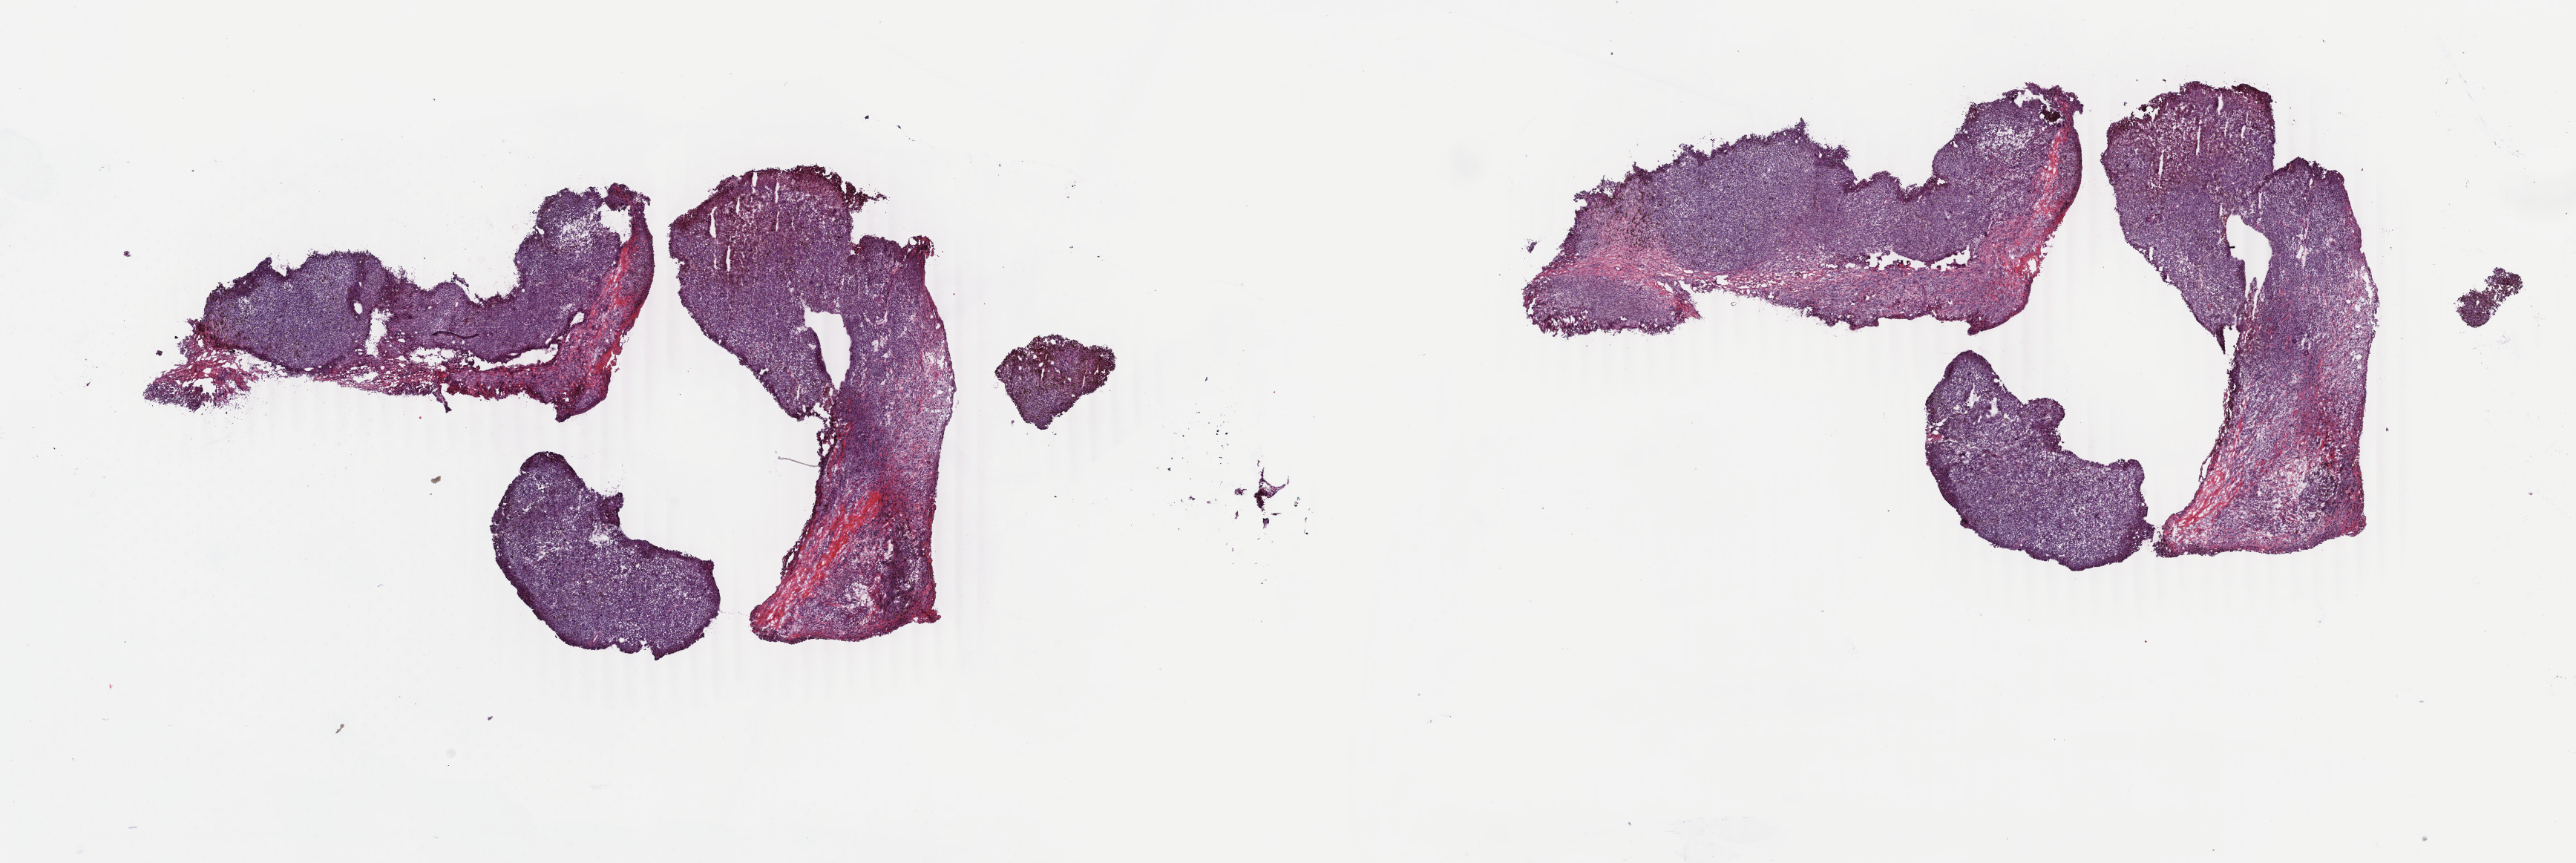
Hematoxylin and eosin (H&E) stained whole-slide image — whole scanned area (about 27.6 x 9.2 mm, from a 40x scan) shown as a low-resolution overview. Frozen section. Metastatic tumour sample, sampled site: connective, subcutaneous and other soft tissues. Male patient; age at initial diagnosis 64 years. Composition of this section per pathologist review: tumour cells 100%, tumour nuclei 91%, normal cells 0%, stromal cells 0%, necrosis 0%. Infiltration values recorded for this section: lymphocyte infiltration 0%, monocyte infiltration 0%, neutrophil infiltration 0%.
This section: metastatic tumour tissue. Patient diagnosis: Malignant melanoma, NOS.